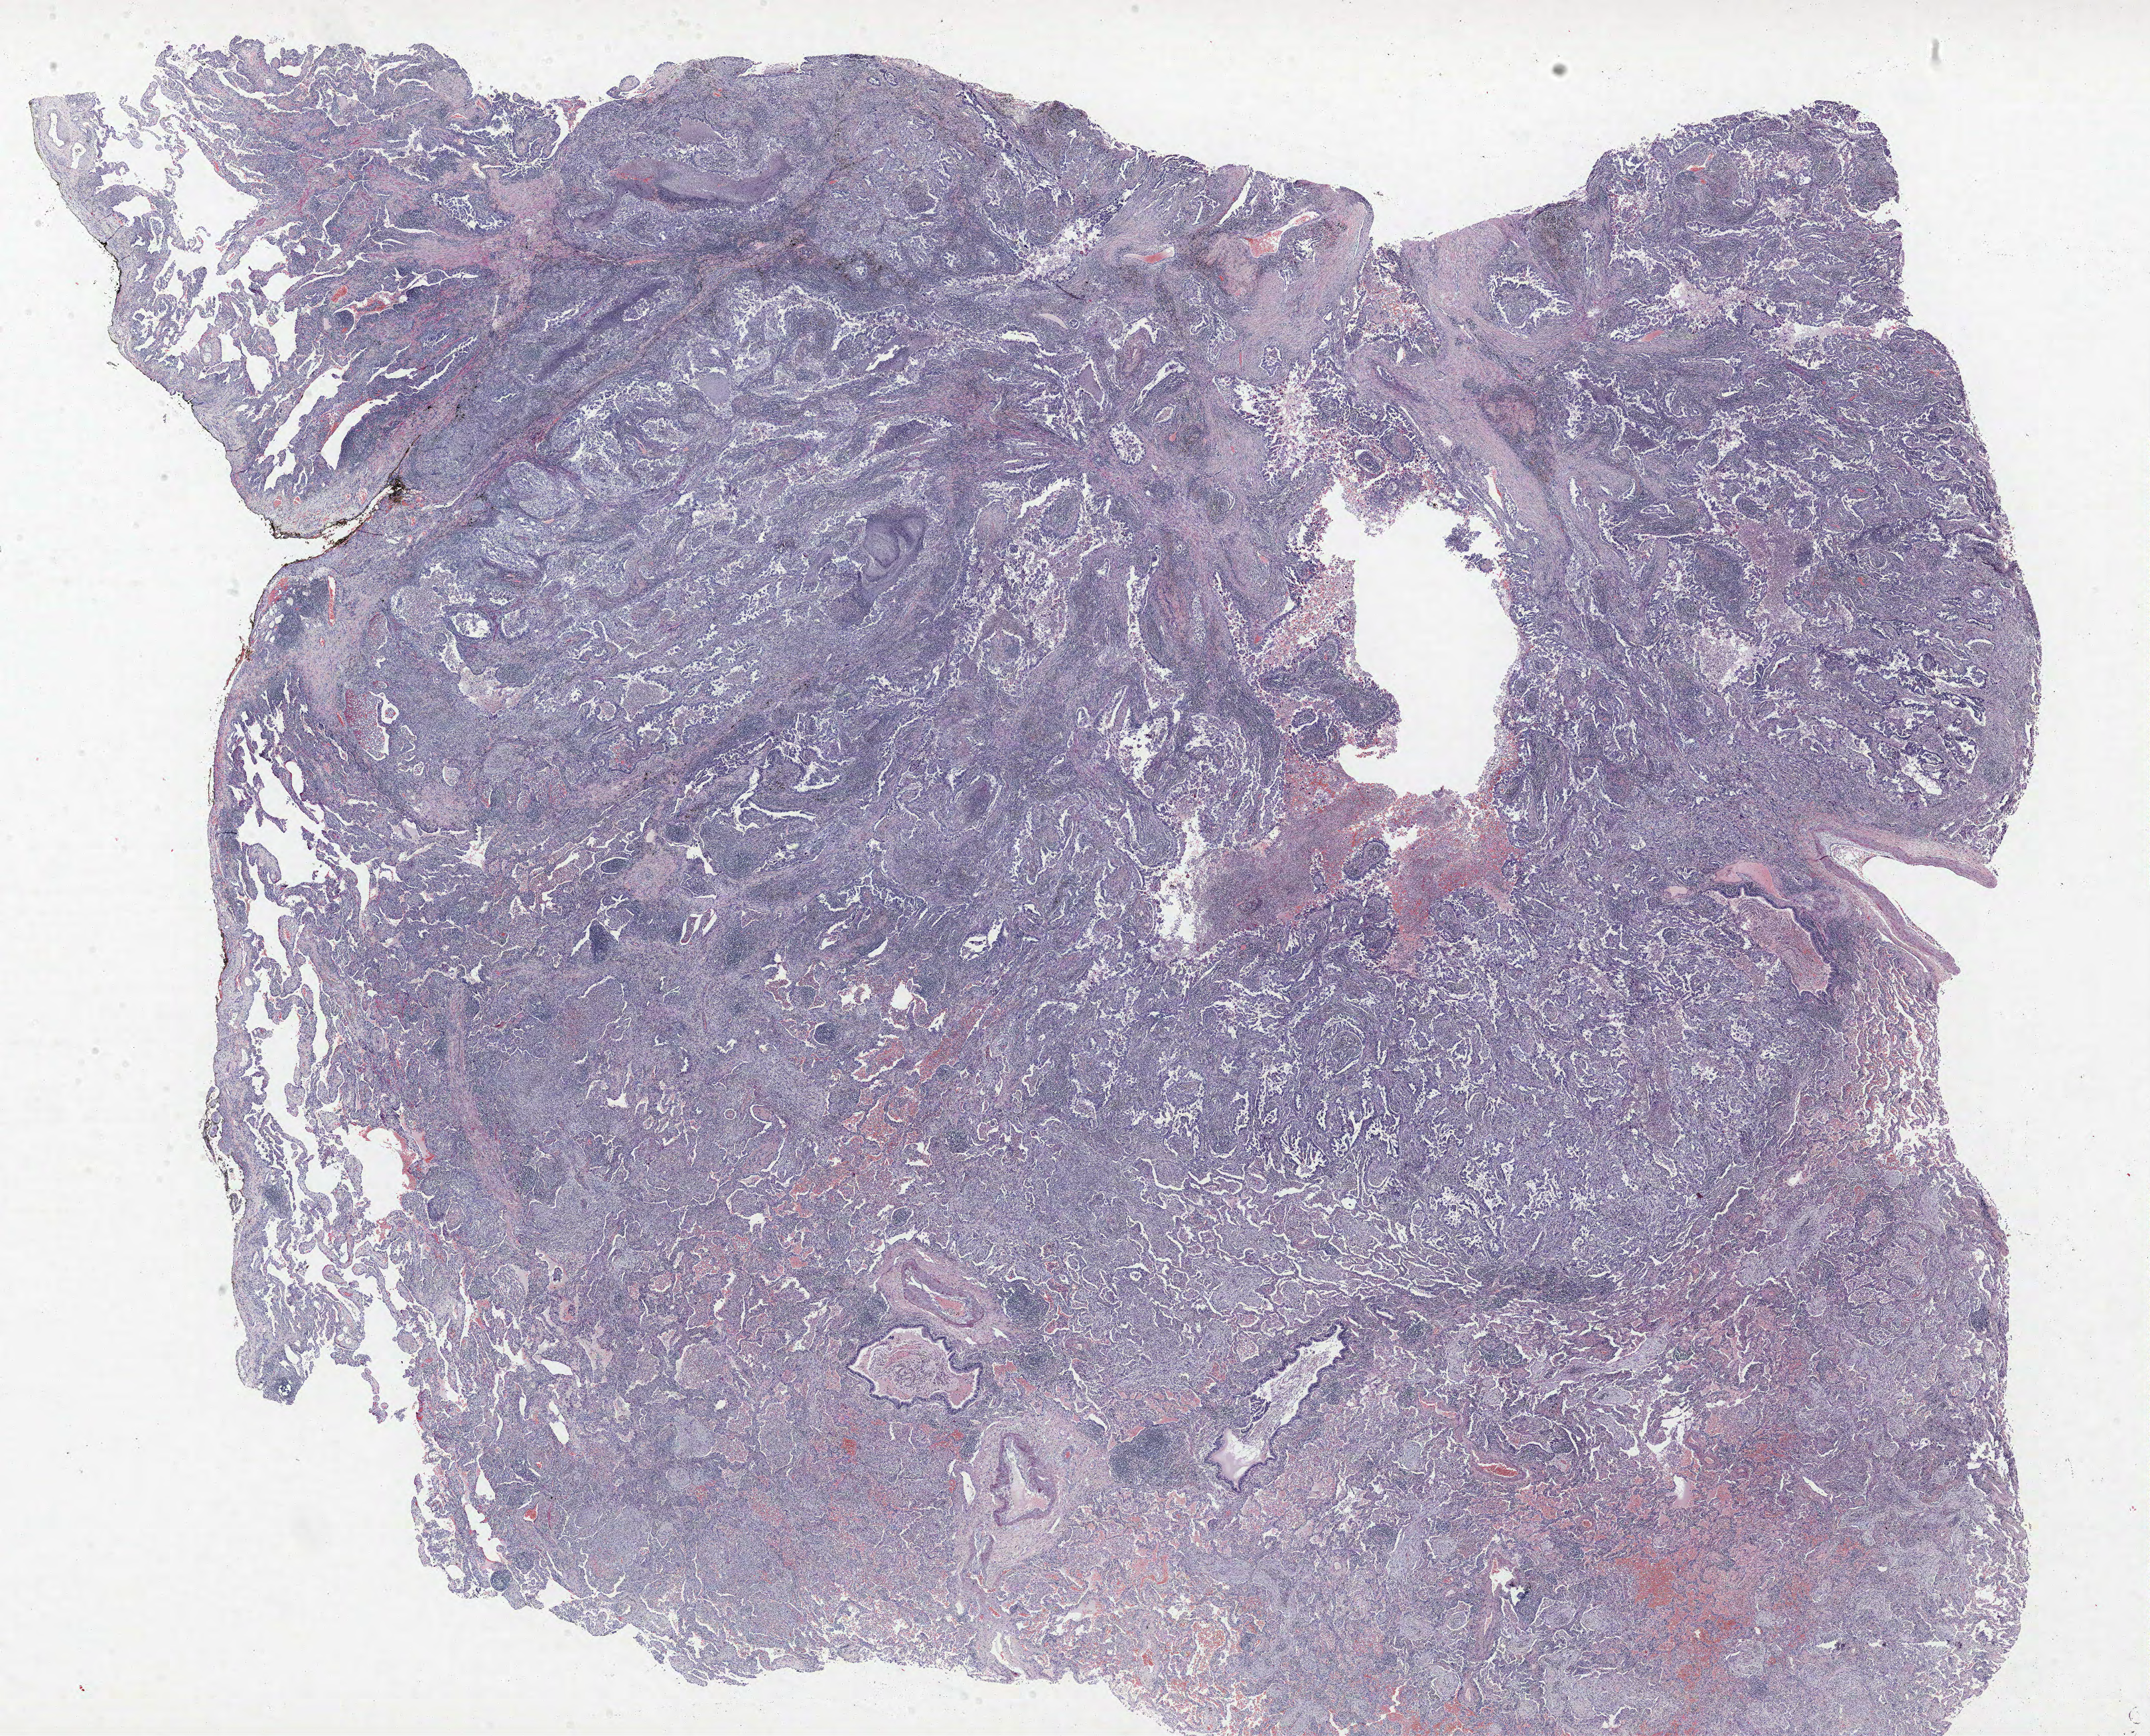
Whole-slide histology image, H&E-stained — a low-resolution overview of the entire scanned area, about 25.9 x 20.9 mm, formalin-fixed paraffin-embedded (FFPE) section, lung. Male, age 61 at enrolment. Former smoker at enrolment. Grade: well differentiated (G1).
- tumour size (pathology): 45 mm
- participant's lung-cancer diagnosis: Adenocarcinoma, NOS (ICD-O-3 8140/3)
- primary tumour location (clinical record): left upper lobe
- stage (AJCC 6th edition): IIIA